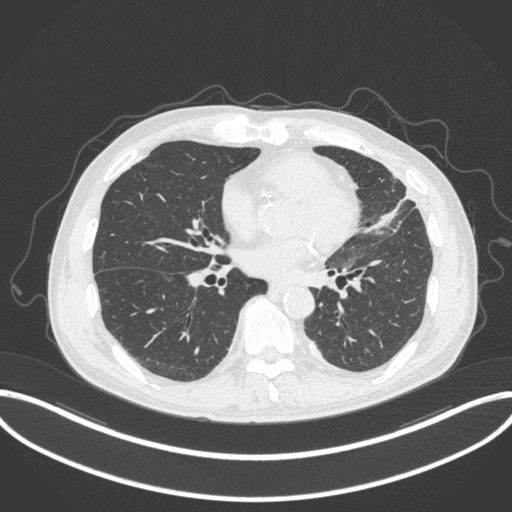
Chest CT, one axial slice; position 144 of 382 along the scan axis; reconstruction kernel B31f; lung window (W 1500 / L -600 HU); 1 mm slice thickness; 512 × 512 image matrix, field of view 415 × 415 mm. Patient: male, 64 years. Case-level facts recorded for this patient, not image findings: clinical TNM (as recorded): T4 N1 M0; histopathological grade: G3.
Annotated regions visible in this slice (rectangle marked by the reading radiologist):
- lung tumour (recorded histology: adenocarcinoma): bounding box [x1, y1, x2, y2] px = [362, 198, 406, 236]